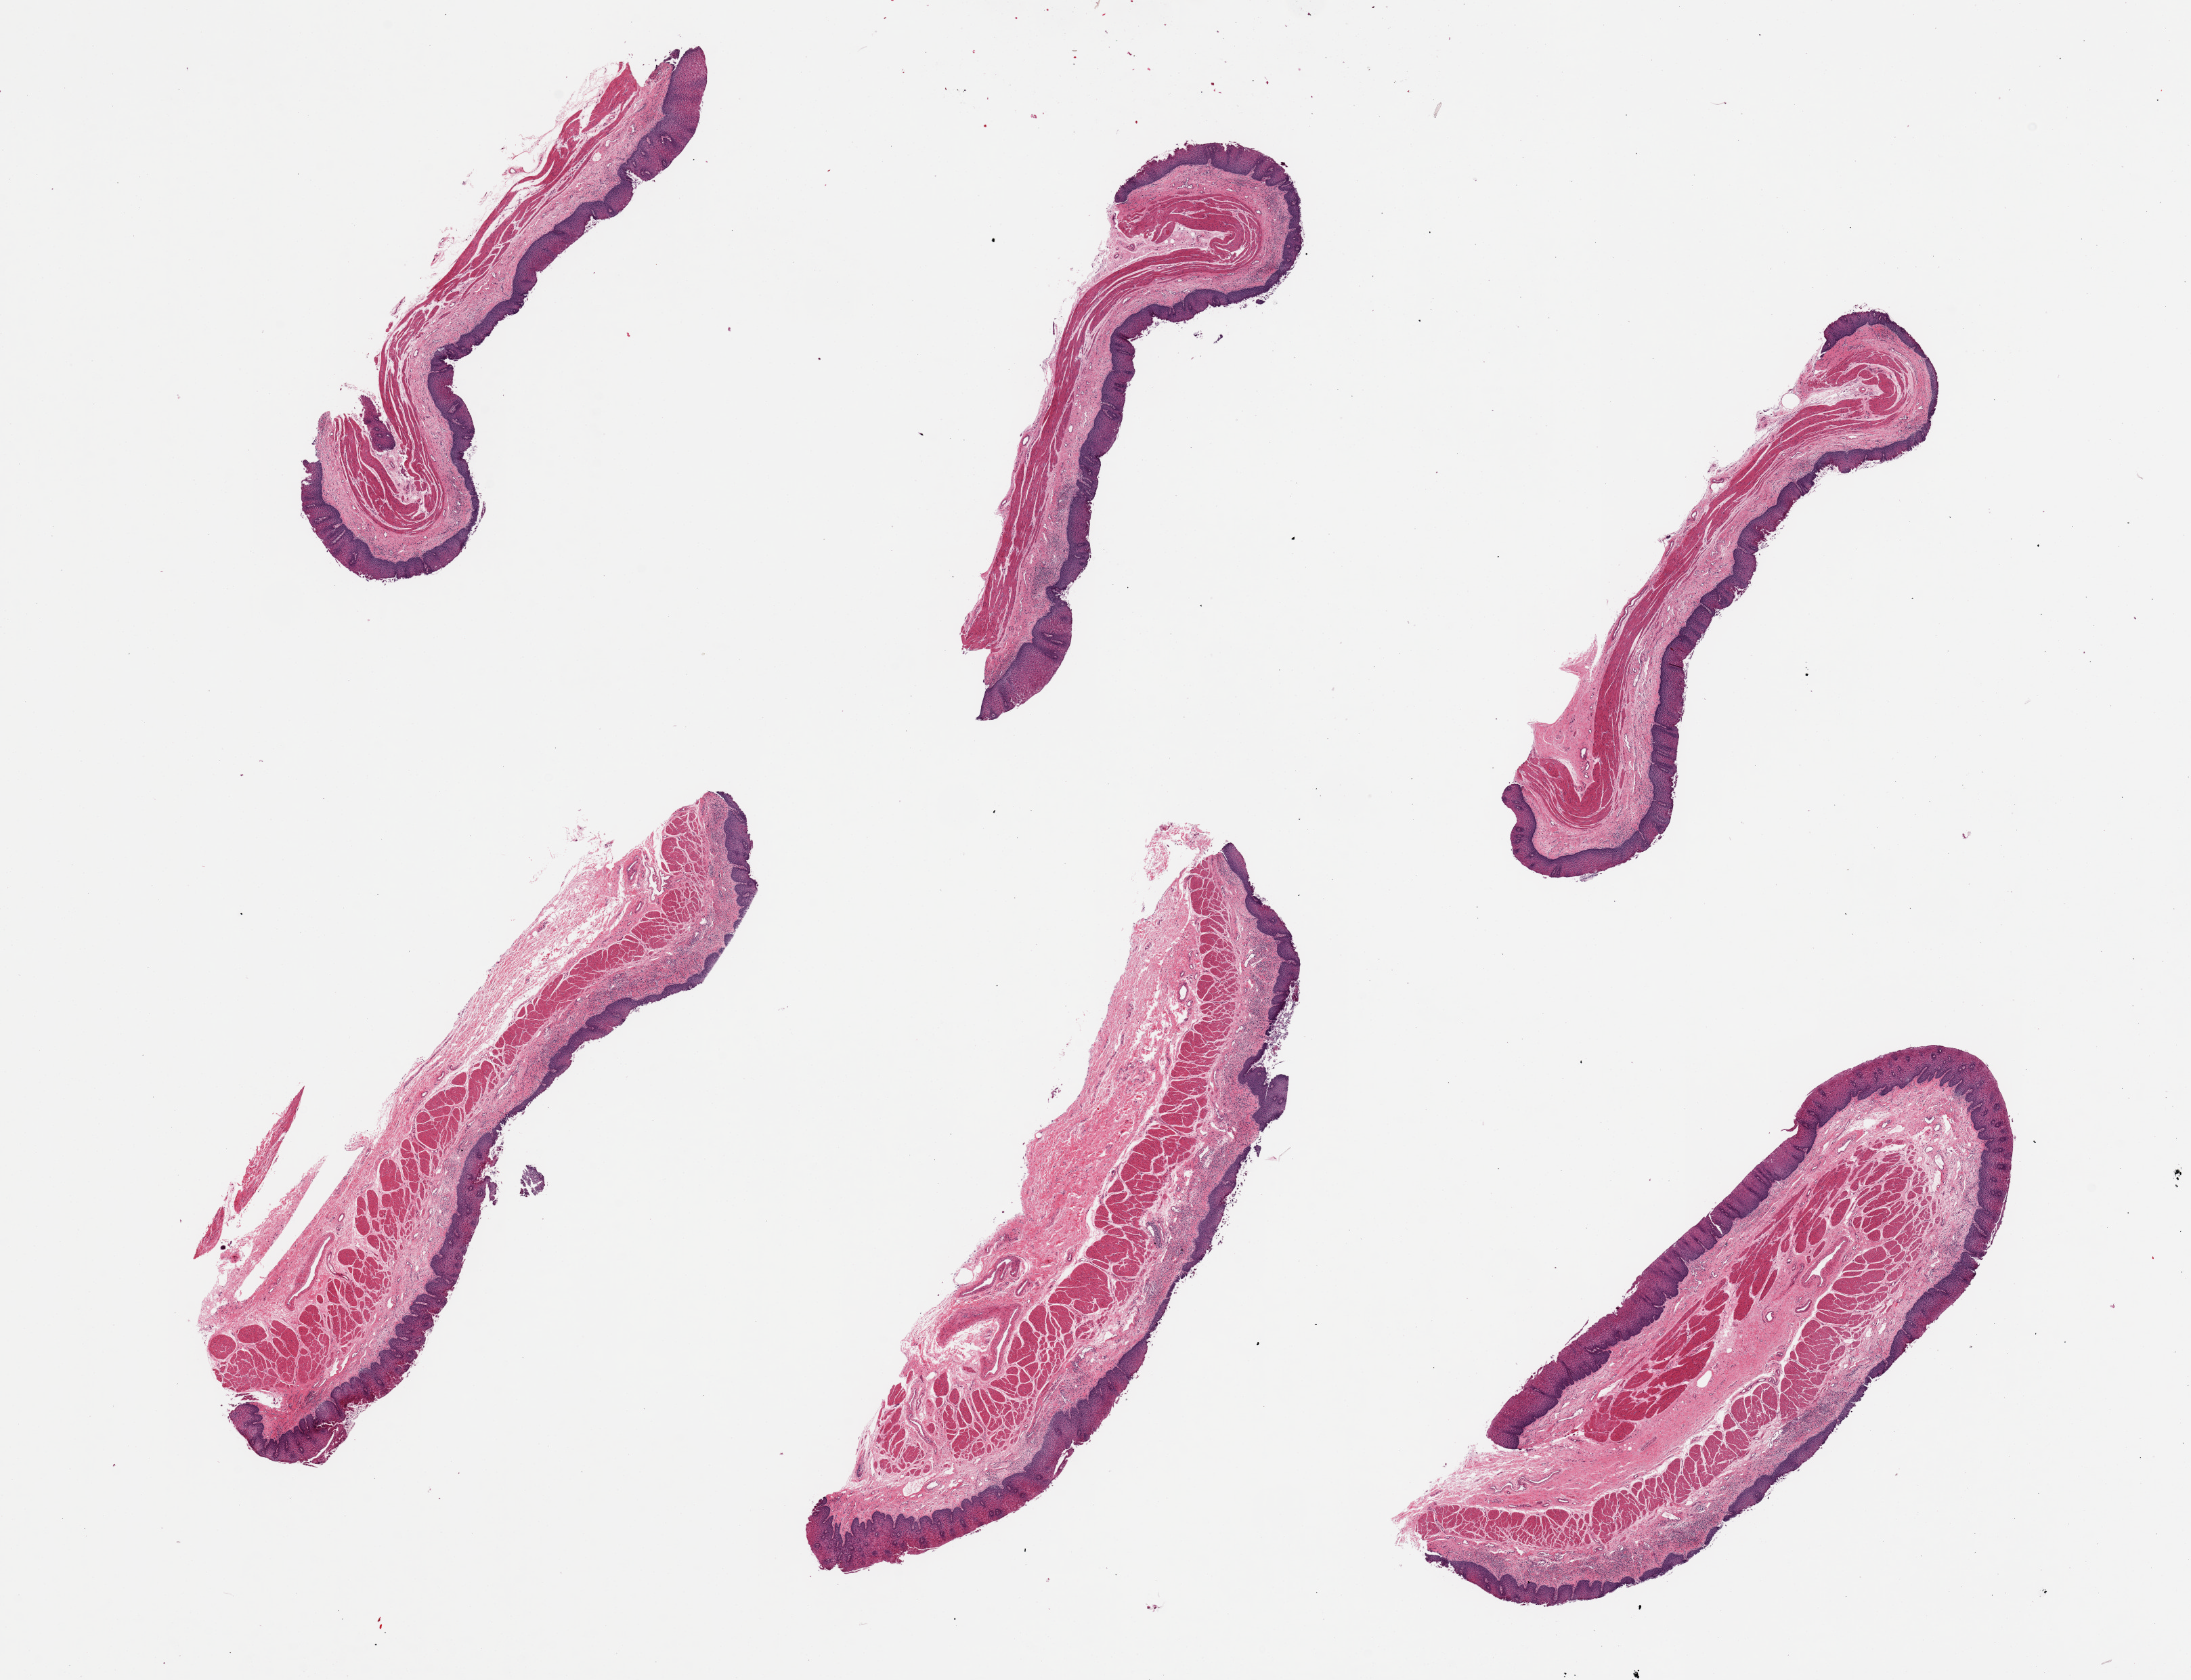
Hematoxylin and eosin (H&E) whole-slide image, brightfield — a low-resolution overview of the entire scanned area, about 25.6 x 19.6 mm; PAXgene-fixed paraffin-embedded (PFPE) section; target tissue: esophageal mucous membrane; donor tissue sample. Male donor.
* reviewer comment on this tissue sample: 6 pieces. Focal surface sloughing. Mild chronic inflammation and squamous hyperplasia